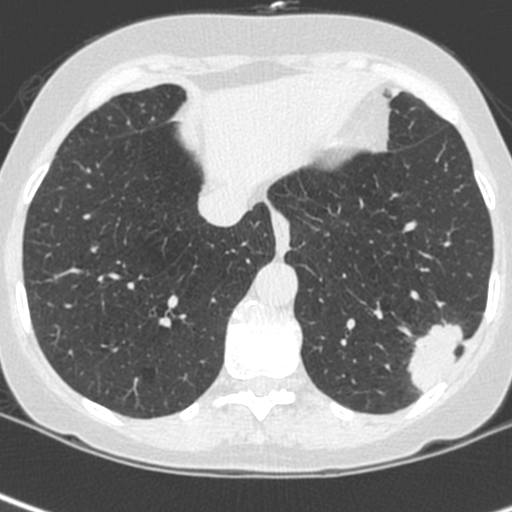
Chest CT (low-dose screening protocol), one axial image; first (baseline) screen; lung window (W 1500 / L -600 HU); standard (soft-tissue) reconstruction kernel (C); slice 175 of 252 in the series. Female participant, aged 56 years at enrolment. Current smoker at enrolment.
Expert reader's lesion annotation, box from (x=404, y=313) to (x=478, y=388) px. Screening reader's record for this exam (one nodule recorded; not confirmed to be the boxed lesion): non-calcified nodule or mass ≥4 mm, left lower lobe, 37 × 29 mm, spiculated (stellate) margins, ground glass attenuation. Participant outcome: lung cancer diagnosed 91 days after this screen — squamous cell carcinoma, NOS, left lower lobe, poorly differentiated (G3), stage IIIA (AJCC 6th edition), 35 mm at pathology.